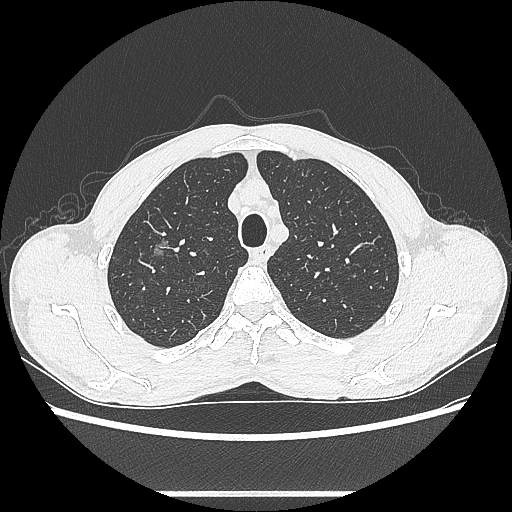
Chest CT, one axial slice. Position 477 of 601 along the scan axis. Reconstruction kernel LUNG. 100 kVp. Lung window (W 1500 / L -600 HU). 0.62 mm slice thickness. 512 × 512 image matrix, field of view 357 × 357 mm. Patient: male, 54 years. From the clinical record (not read from this slice): clinical TNM (as recorded): T1a N0 M0.
Annotated regions visible in this slice (rectangle marked by the reading radiologist):
- lung tumour (recorded histology: adenocarcinoma): box from (x=148, y=233) to (x=175, y=262) px